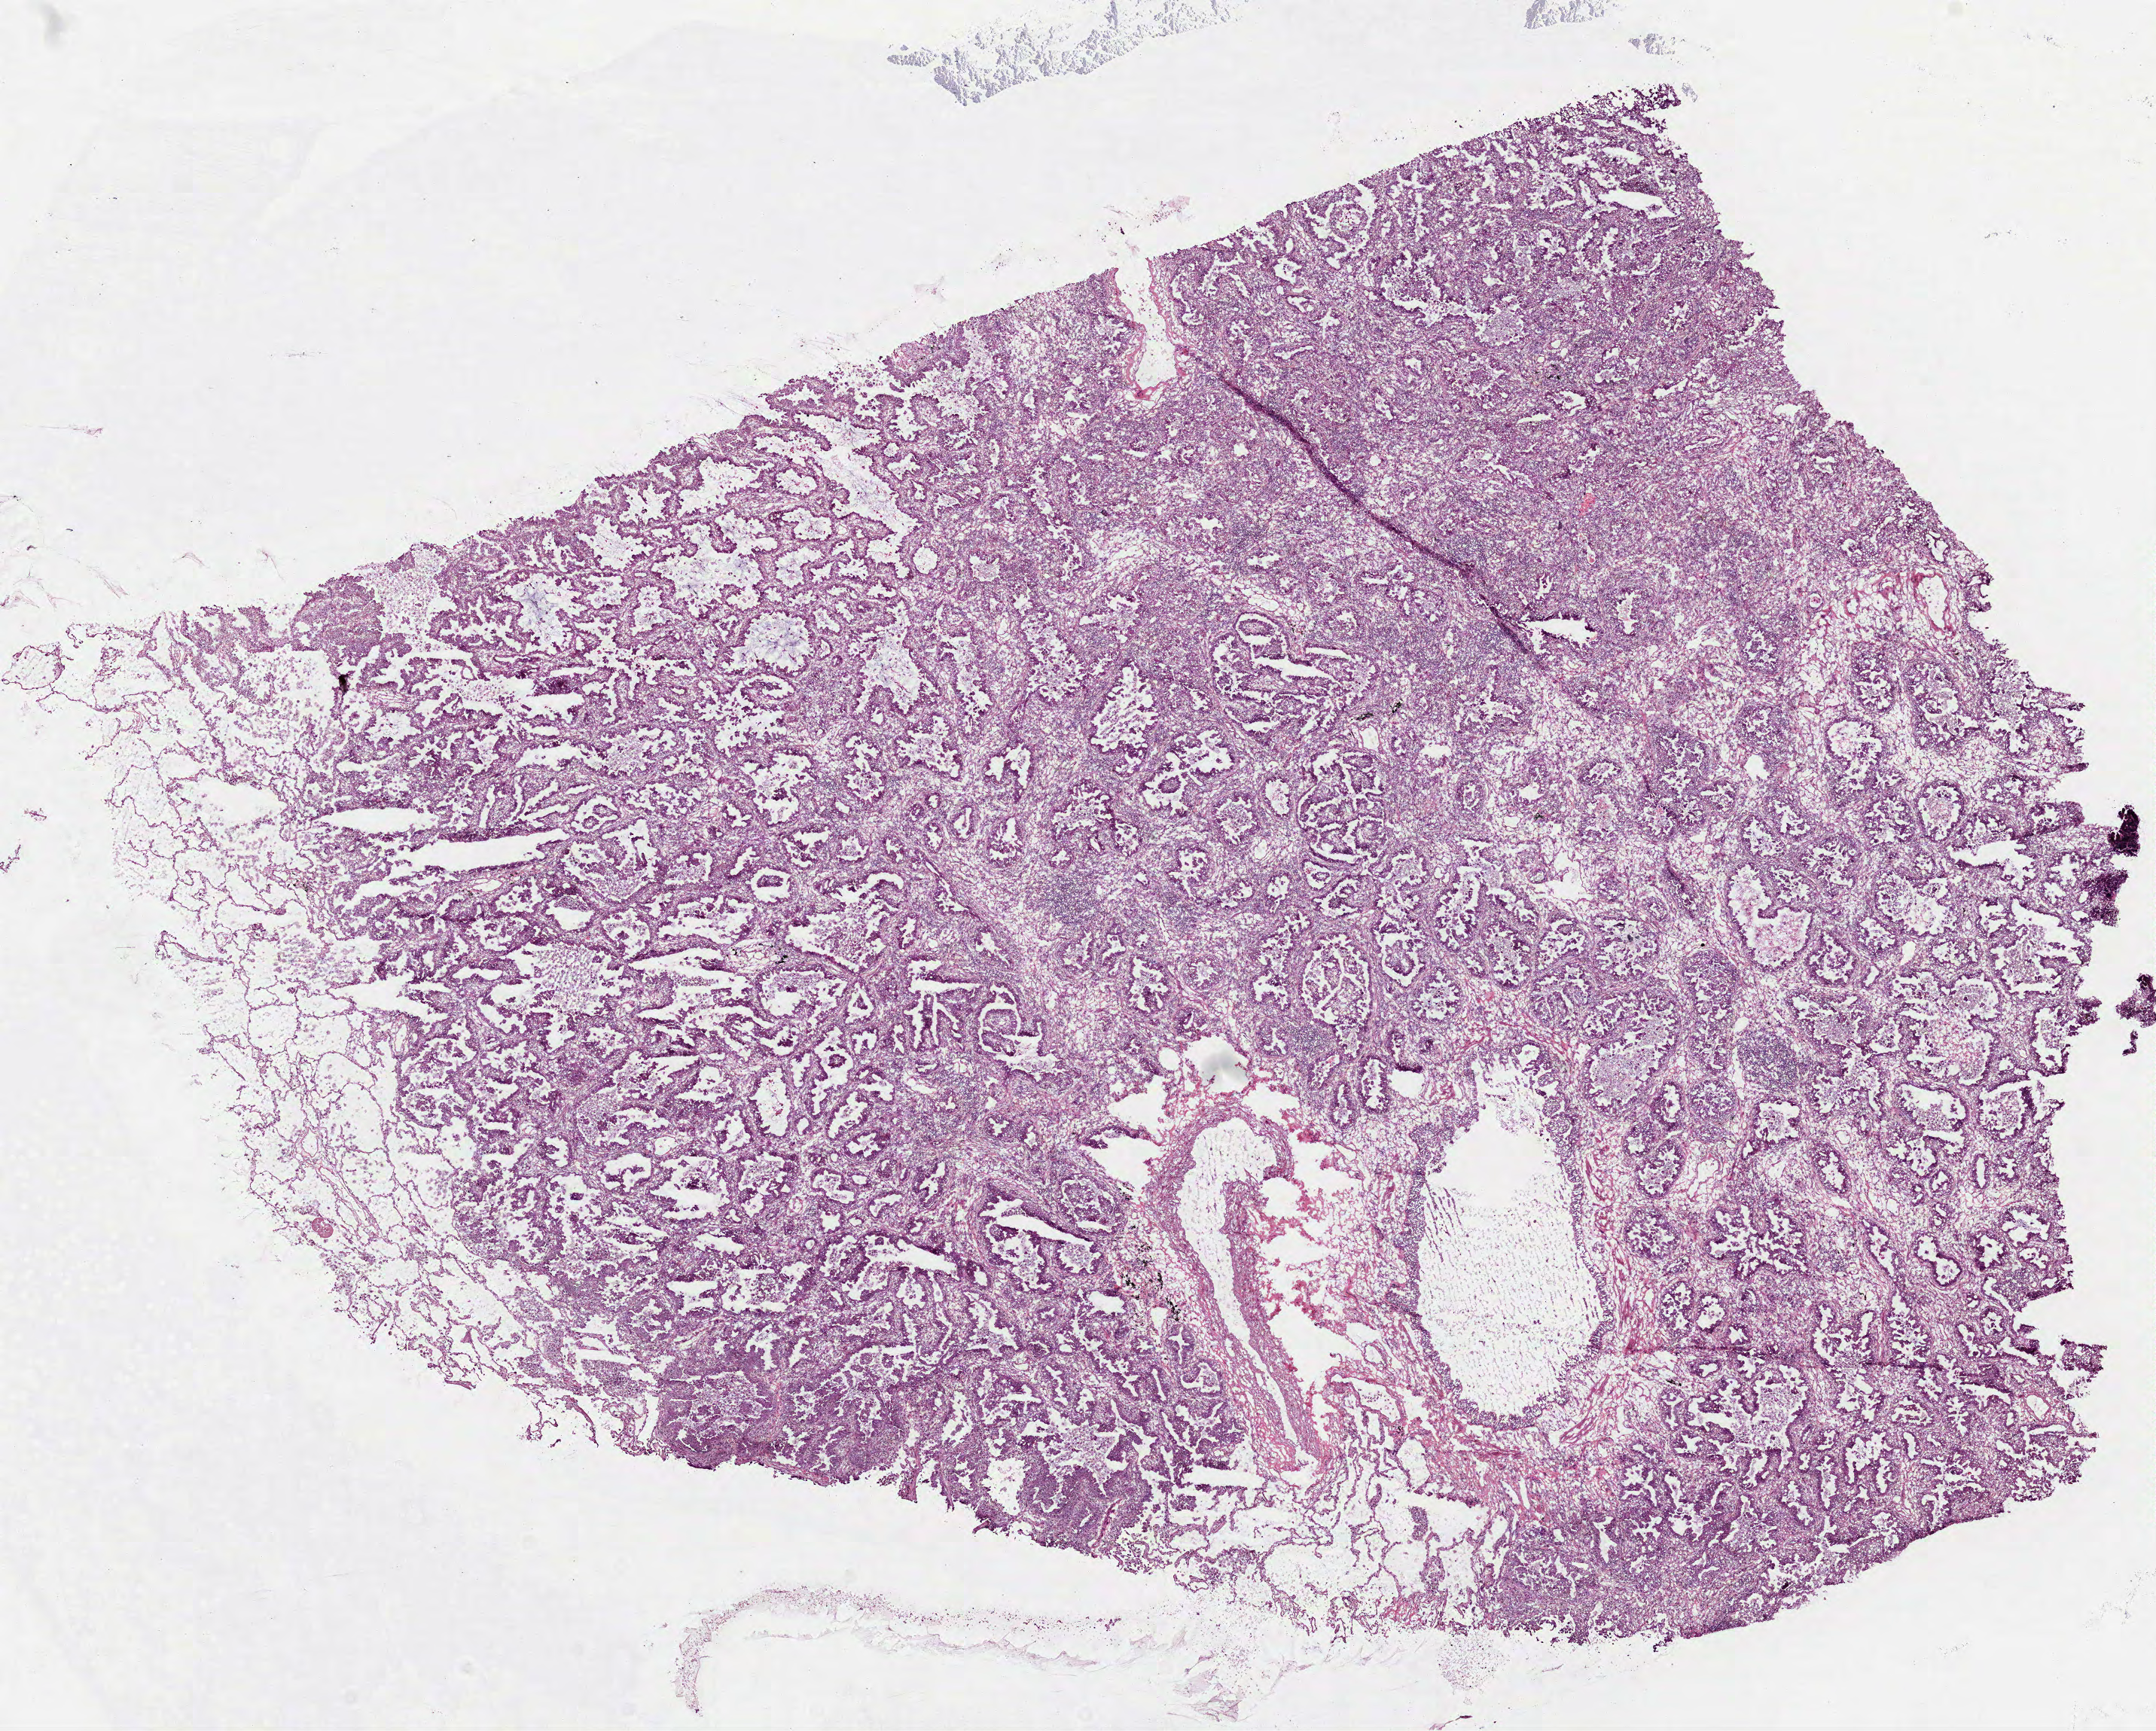
H&E-stained whole-slide image, shown as a low-resolution overview of the whole scanned area (about 11.5 x 9.3 mm, from a 40x scan), frozen section from the top of the tissue portion, sample: primary tumour, lung. Female, age 84 years at initial diagnosis. Composition of this section per pathologist review: tumour cells 65%, tumour nuclei 75%, normal cells 10%, stromal cells 20%, necrosis 5%.
- pathologic diagnosis: Adenocarcinoma, NOS (upper lobe, lung)
- AJCC pathologic stage: I (6th edition)